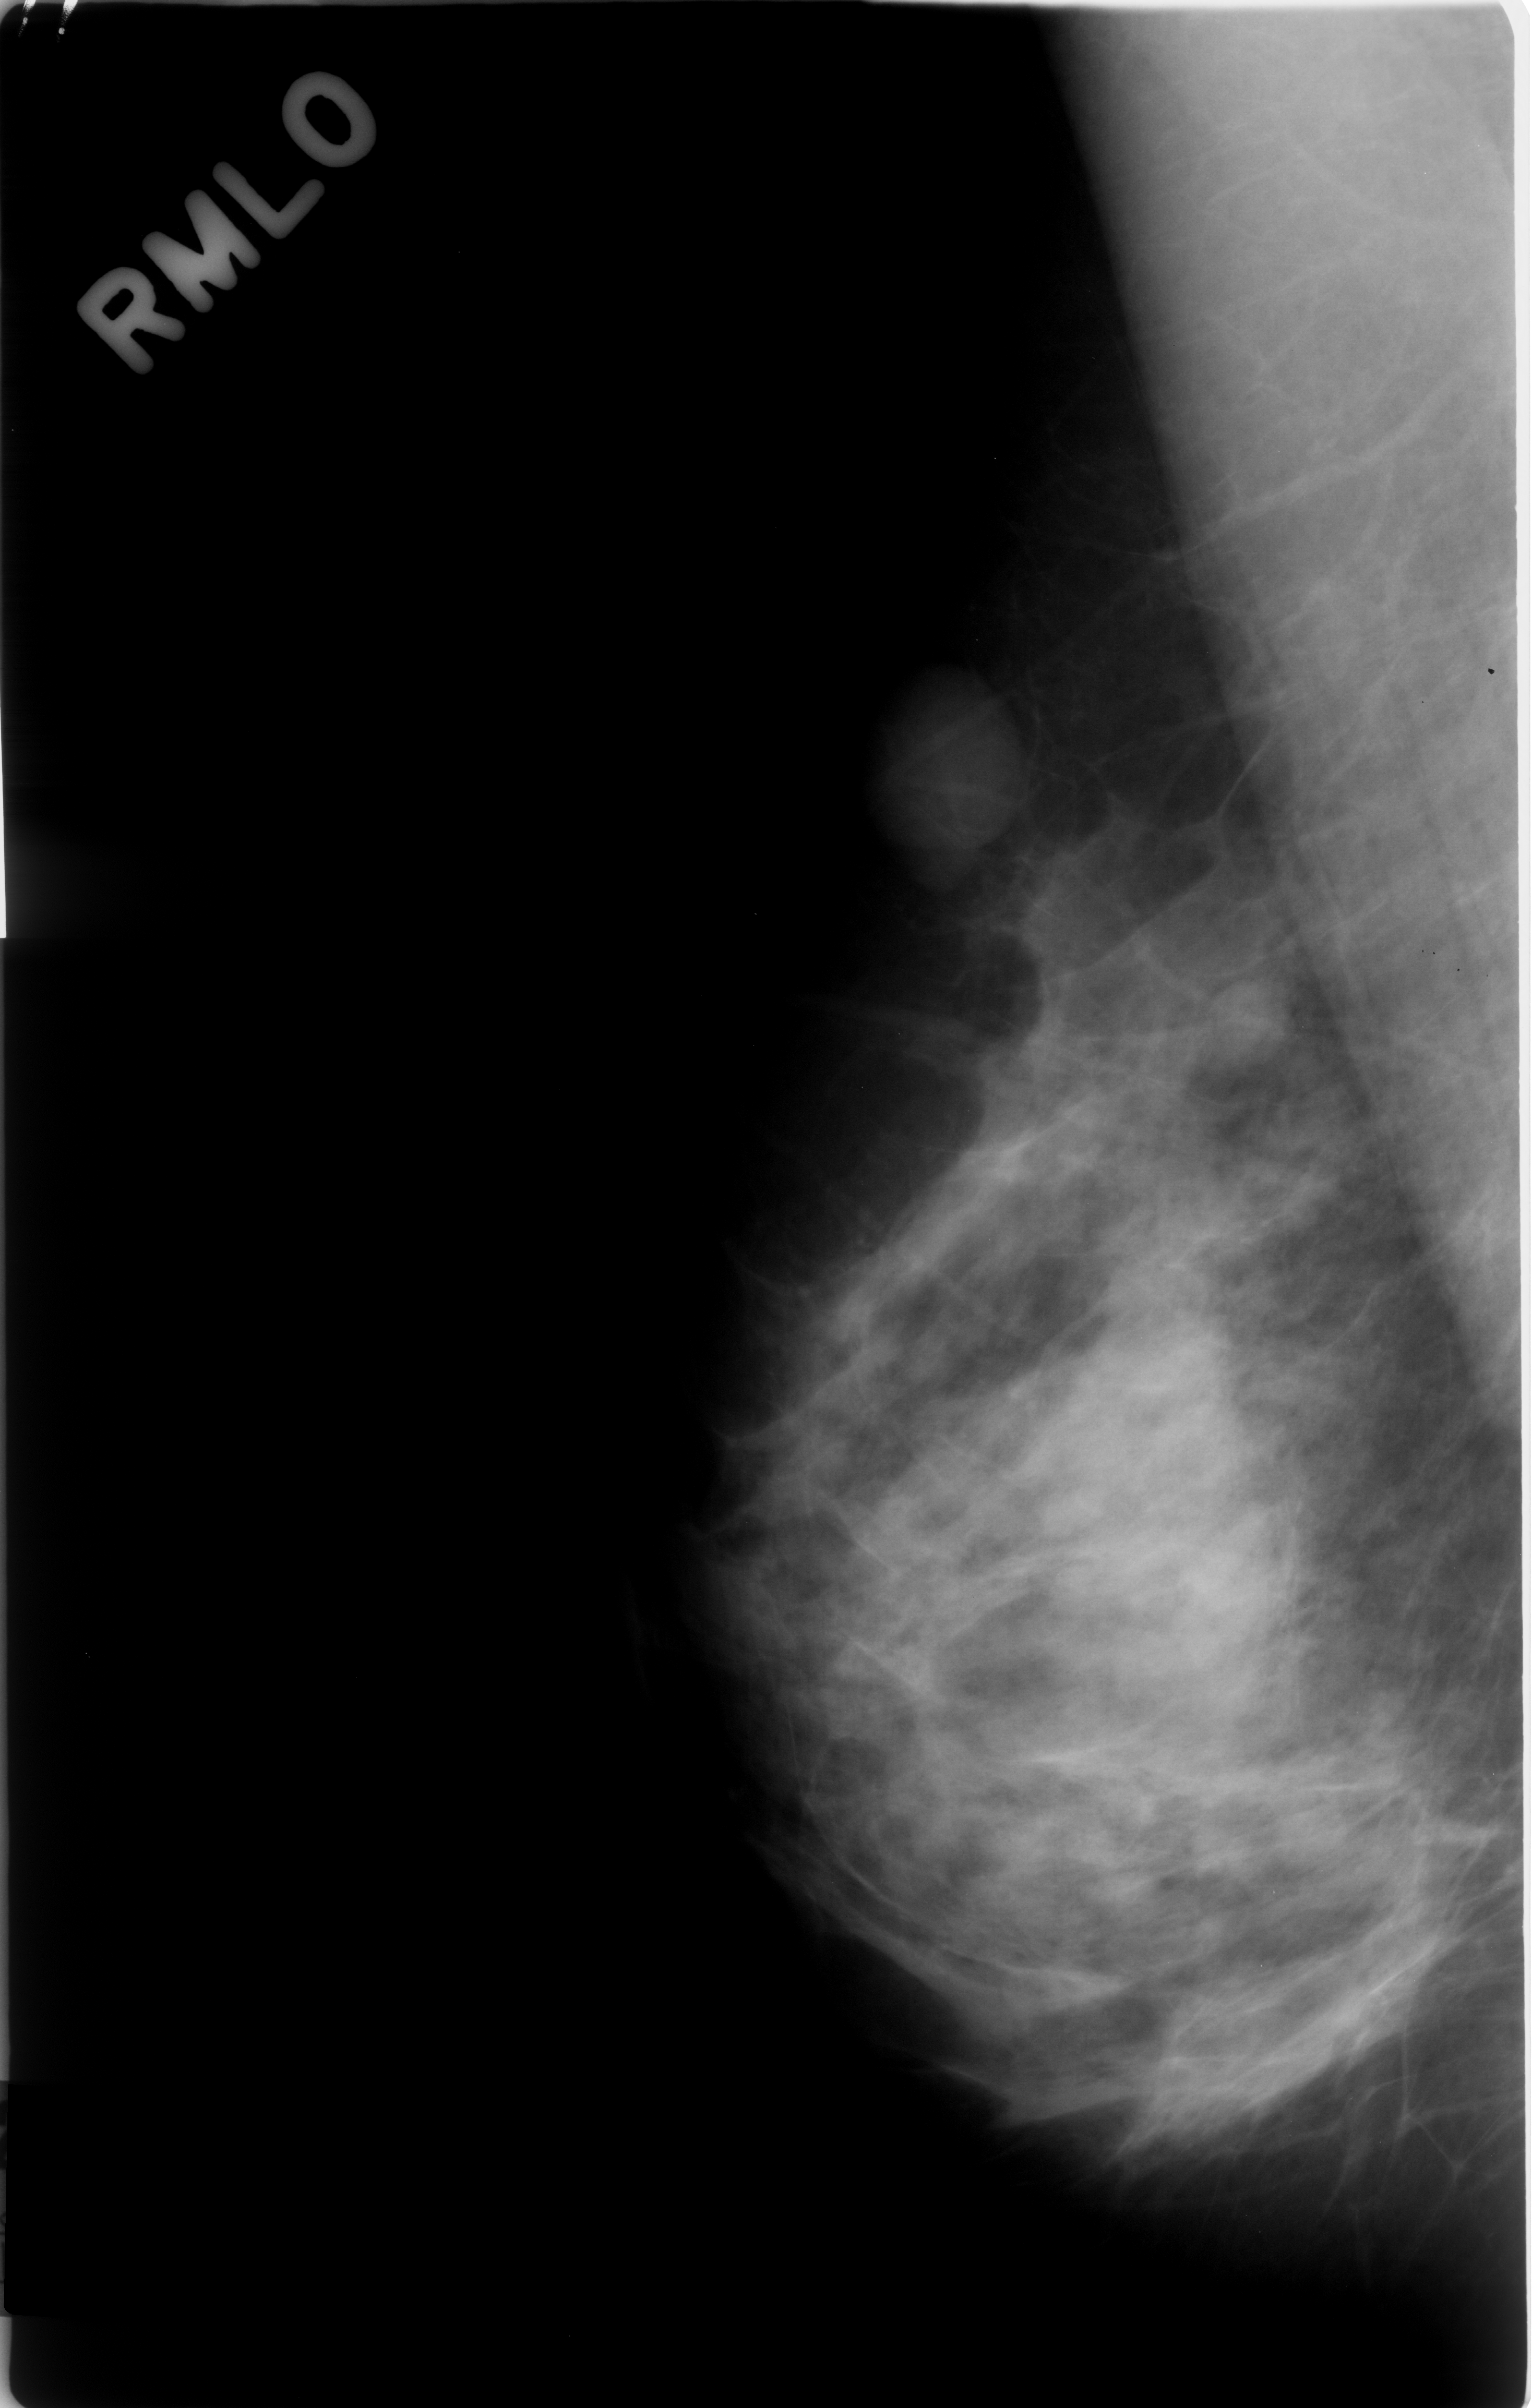
Scanned film-screen mammogram, right breast, MLO view.
Finding: mass, shape lobulated, margins circumscribed; BI-RADS assessment category 3; subtlety rating 4 on a 1 (subtle) to 5 (obvious) scale; pathology (as recorded): benign.